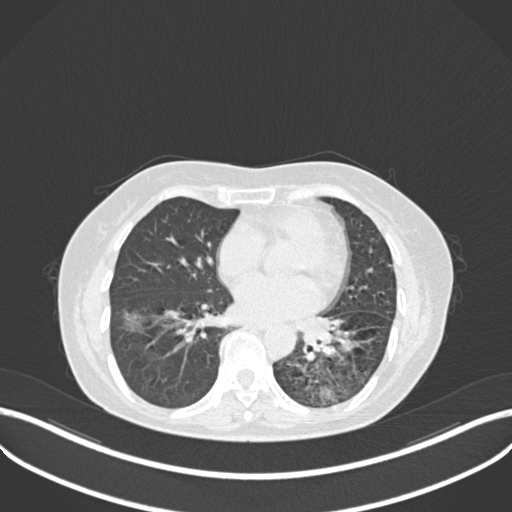
Chest CT, one axial slice; slice 111 of 270 in the series (ordered by position); reconstruction kernel B30f; 120 kVp; lung window (W 1500 / L -600 HU); 1 mm slice thickness; 512 × 512 image matrix, field of view 400 × 400 mm. Patient: female, 63 years. From the clinical record (not read from this slice): clinical TNM (as recorded): T1b N0 M0.
Annotated regions visible in this slice (rectangle marked by the reading radiologist):
- lung tumour (recorded histology: adenocarcinoma): bounding box (x1, y1, x2, y2) in pixels: (294, 311, 356, 364)